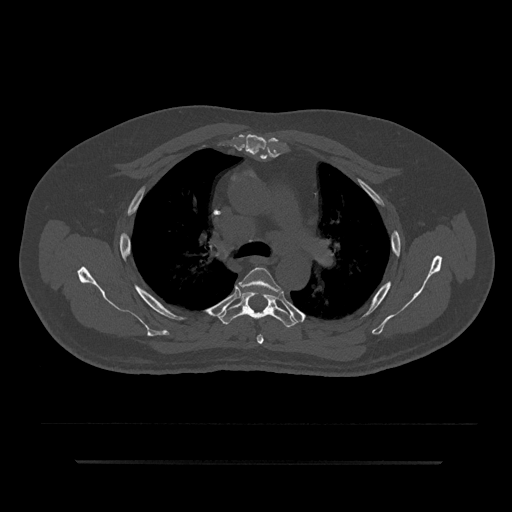
CT including the spine, one axial slice; position 591 of 797 along the scan axis; reconstruction kernel Br40s/3; 120 kVp; bone window (W 1800 / L 400 HU); 512 × 512 image matrix. Patient: male, 59 years. From the clinical record (not read from this slice): primary cancer: bile ducts.
Outlined on this slice (semi-automatic segmentation, software-assisted and operator-edited):
- T4 vertebra: bounding box (x1, y1, x2, y2) in pixels: (239, 267, 281, 345)
- T5 vertebra: (218, 291, 298, 327)